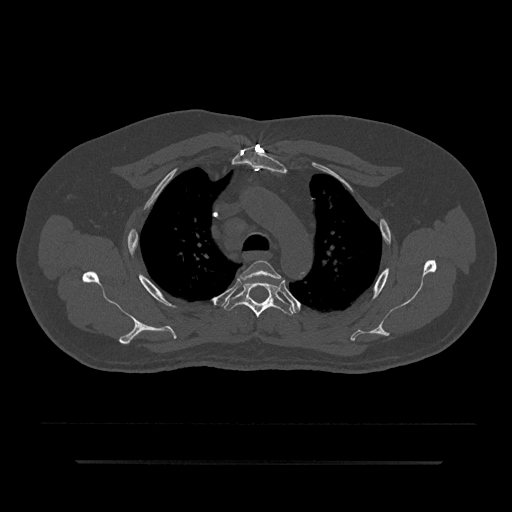
CT including the spine, one axial slice. Slice 629 of 797 in the series (ordered by position). Reconstruction kernel Br40s/3. 120 kVp. Bone window (W 1800 / L 400 HU). 0.5 mm slice thickness. 512 × 512 image matrix, field of view 464 × 464 mm. Patient: male, 59 years. From the clinical record (not read from this slice): primary cancer: bile ducts; vertebrae with lytic lesions (as recorded): T10.
Outlined on this slice (semi-automatic segmentation, software-assisted and operator-edited):
- T3 vertebra: bounding box [x1, y1, x2, y2] px = [240, 260, 283, 282]
- T4 vertebra: [223, 282, 295, 318]